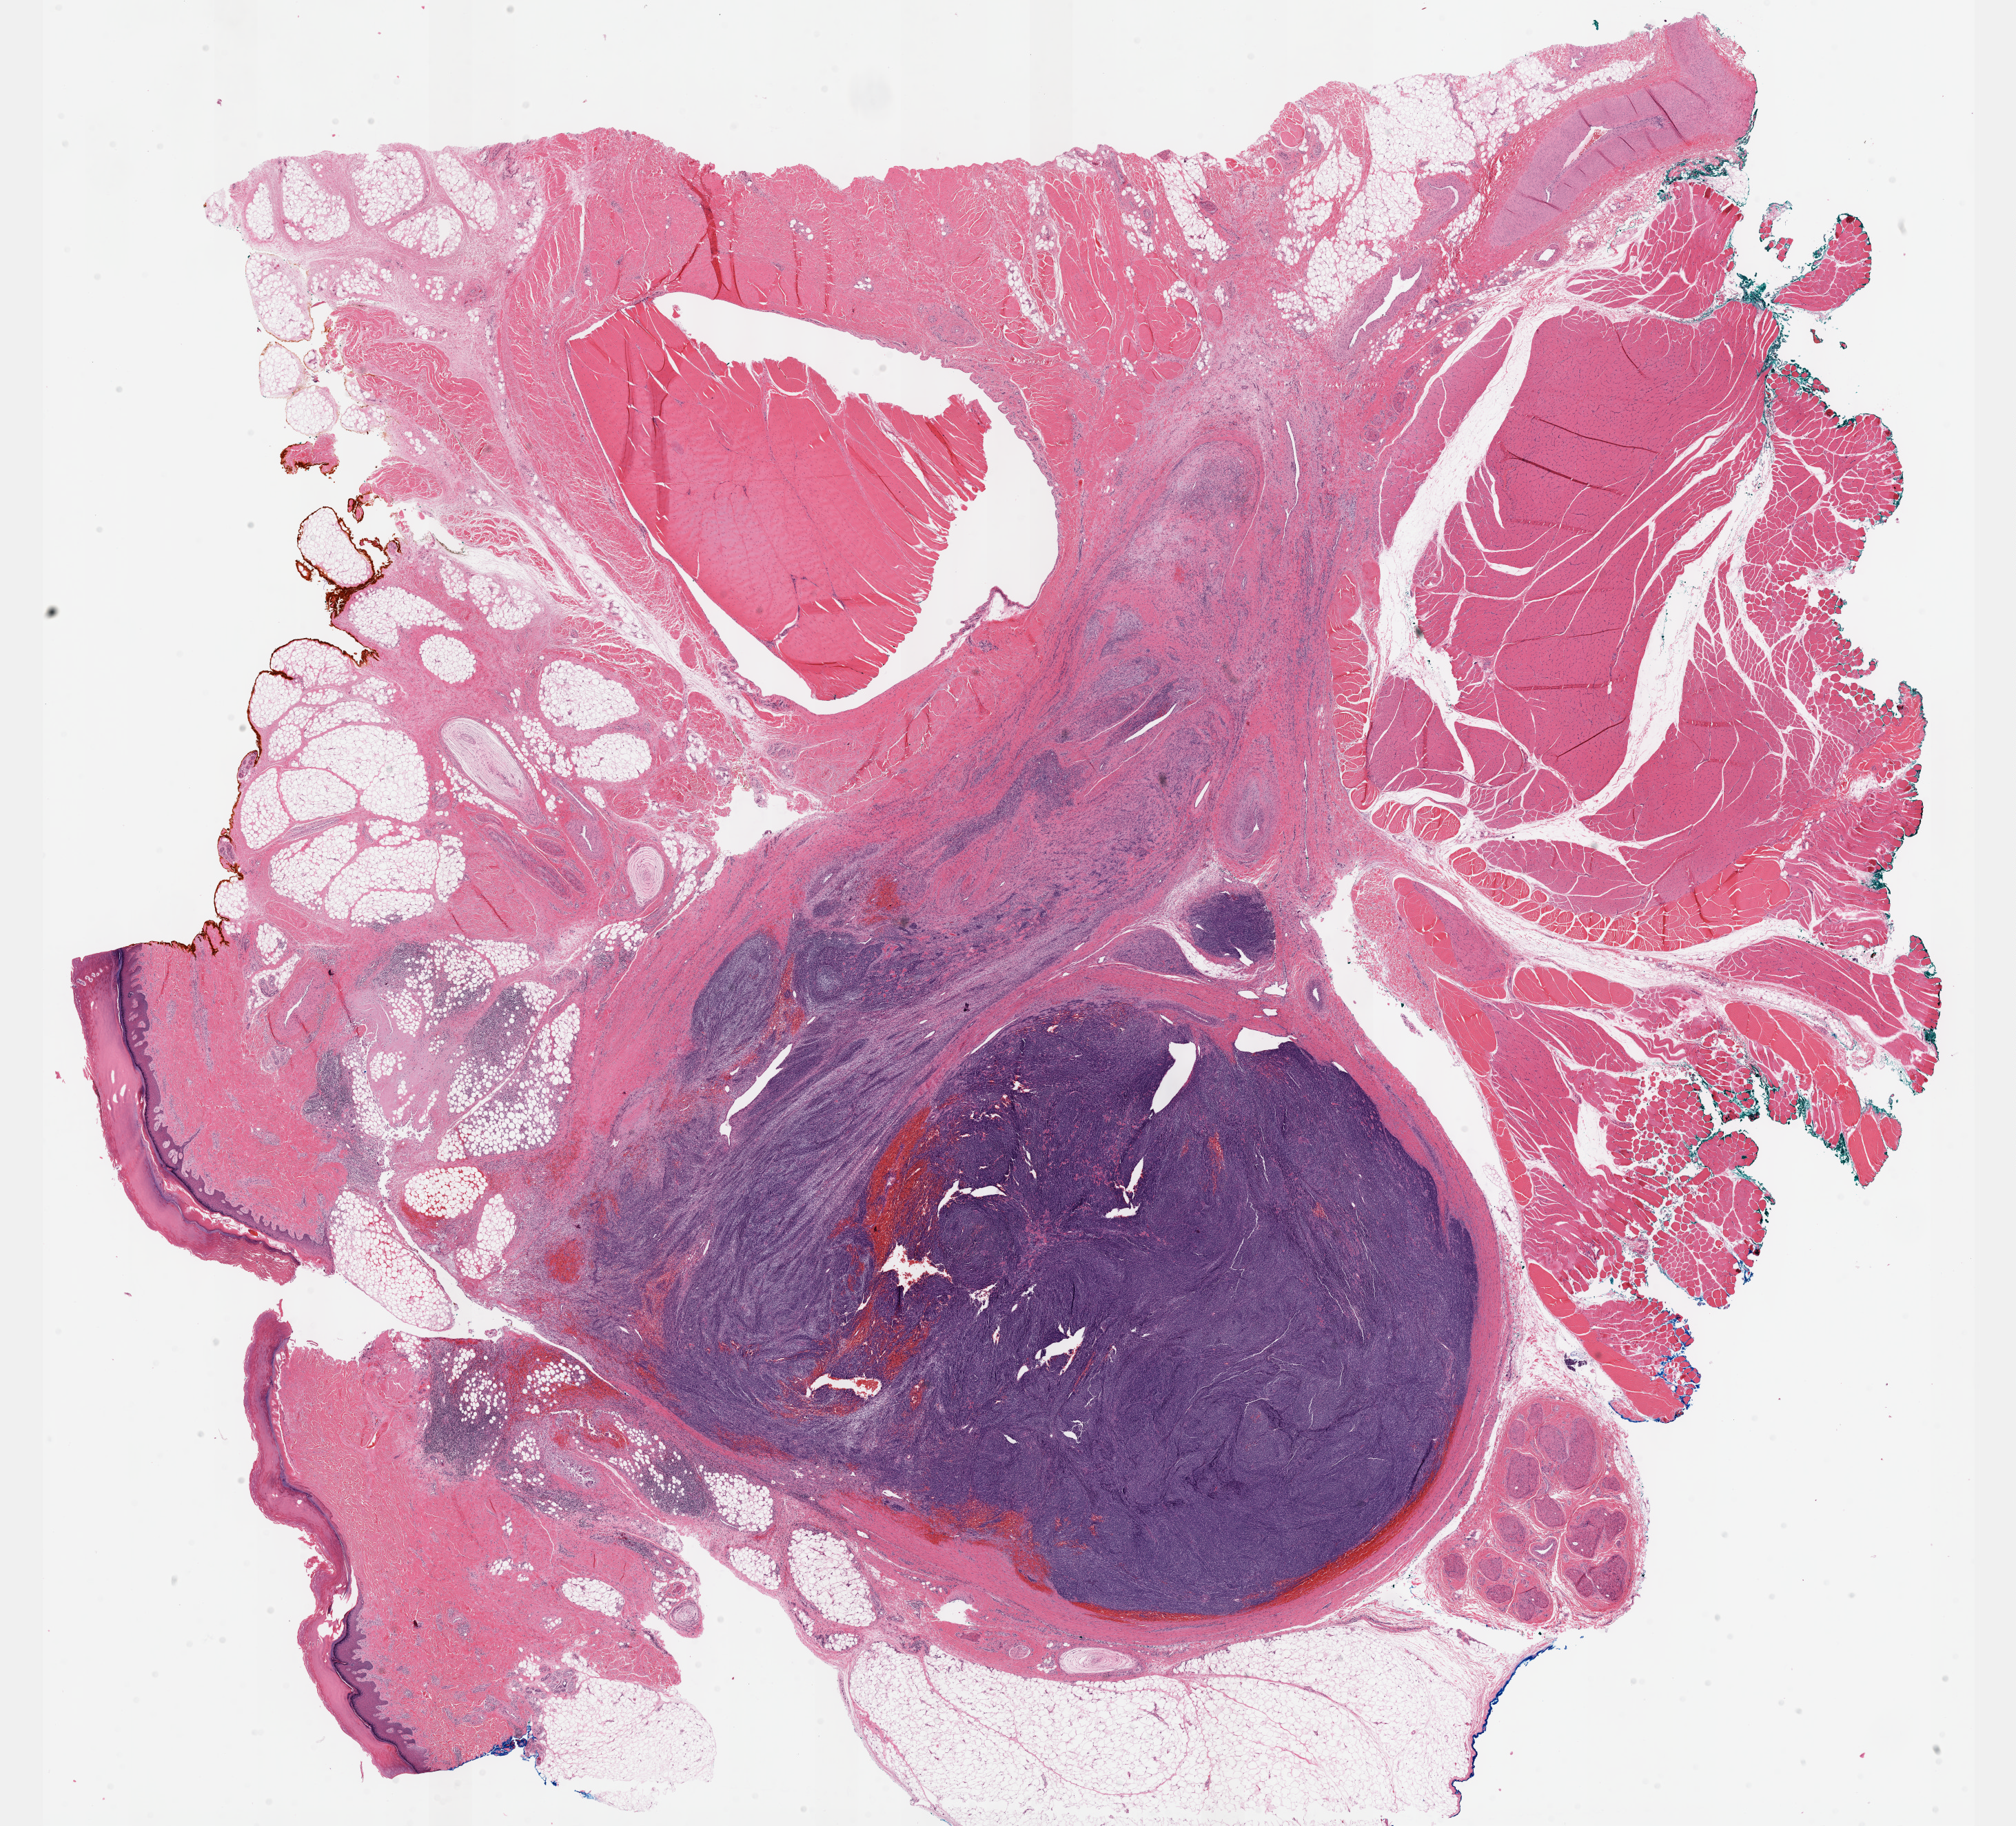
H&E whole-slide image — whole scanned area (about 23.6 x 21.4 mm) shown as a low-resolution overview; formalin-fixed paraffin-embedded (FFPE) diagnostic section; sample: primary tumour, connective, subcutaneous and other soft tissues. Female, age 24 years at initial diagnosis.
• diagnosis: Synovial sarcoma, biphasic (connective, subcutaneous and other soft tissues of lower limb and hip)